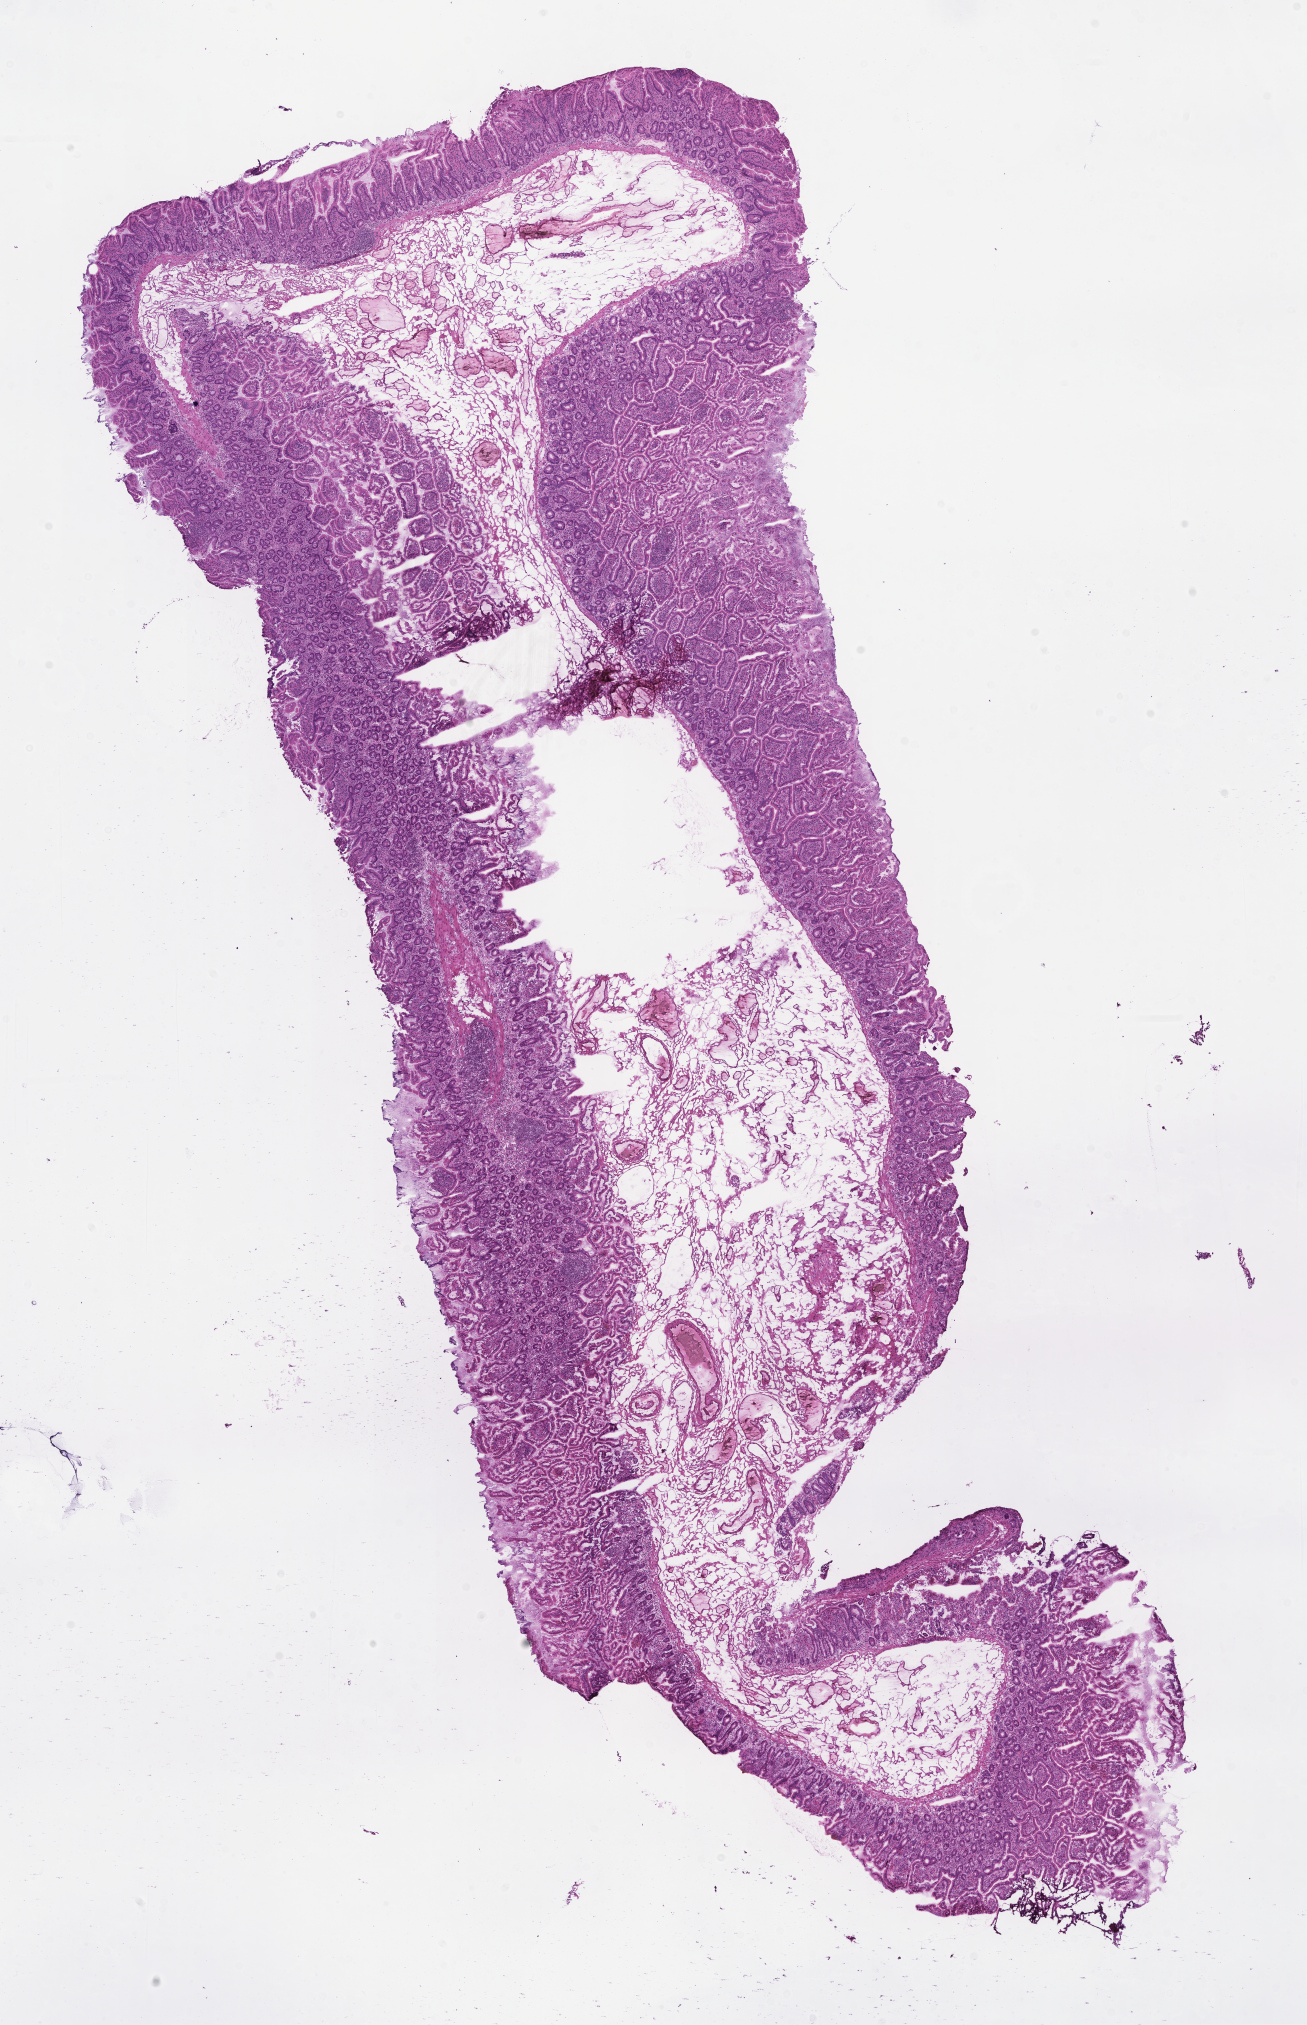
Whole-slide image, haematoxylin and eosin stain — shown as a low-resolution overview of the whole scanned area (about 10.6 x 16.4 mm). Frozen section (tissue freezing medium). Normal-tissue sample (non-tumor) from a patient with cholangiocarcinoma. Male patient; age at initial diagnosis 73 years. Pathologist review of this section (percent, as recorded): tumor cells 0%, tumor nuclei 0%, stromal cells 0%, necrosis 0%, normal cells 100%. Infiltration values recorded for this section: lymphocyte infiltration 15%, monocyte infiltration 2%, neutrophil infiltration 10%.
This section: non-tumor tissue sample; the patient's diagnosis is given above.